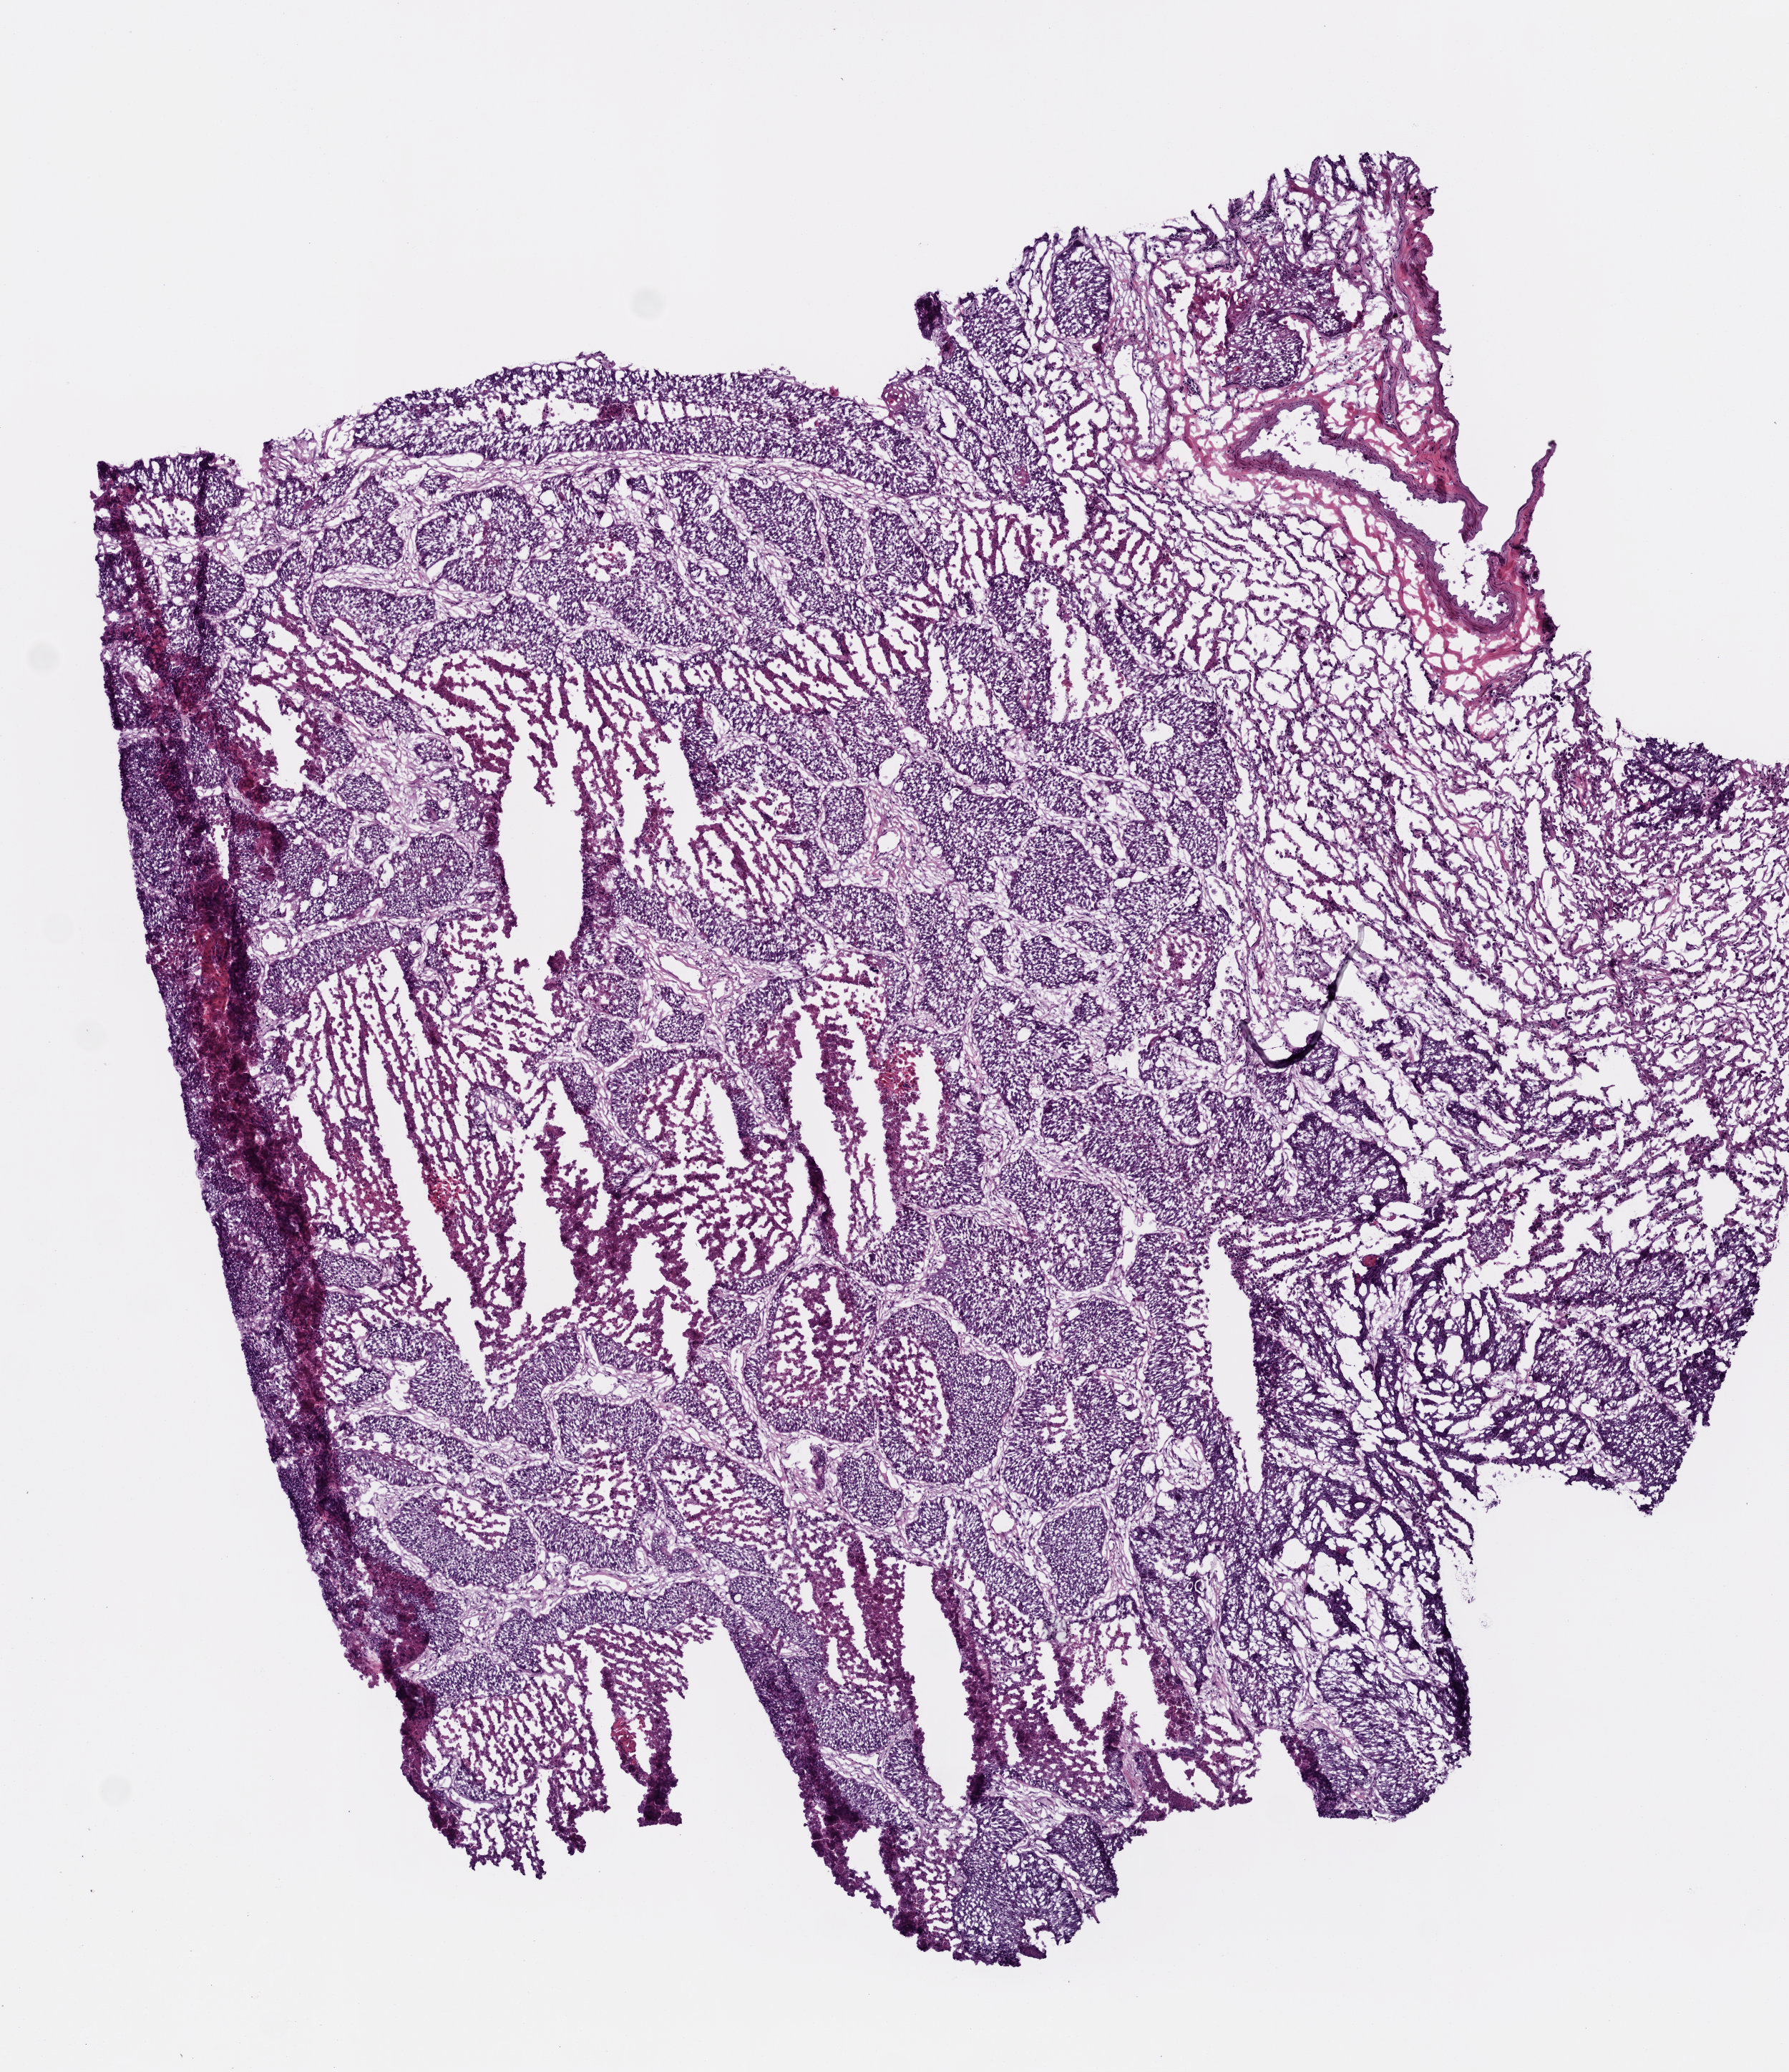
Hematoxylin and eosin (H&E) stained whole-slide image — low-resolution overview of the scanned area, about 5.0 x 5.8 mm (acquisition: 20x scan). Frozen section. Sample: primary tumour, lung. Male, age 50 years at initial diagnosis. Pathologist review of this section (percent, as recorded): tumour cells 60%, tumour nuclei 80%.
Histologic diagnosis: Squamous cell carcinoma, NOS (lower lobe, lung).